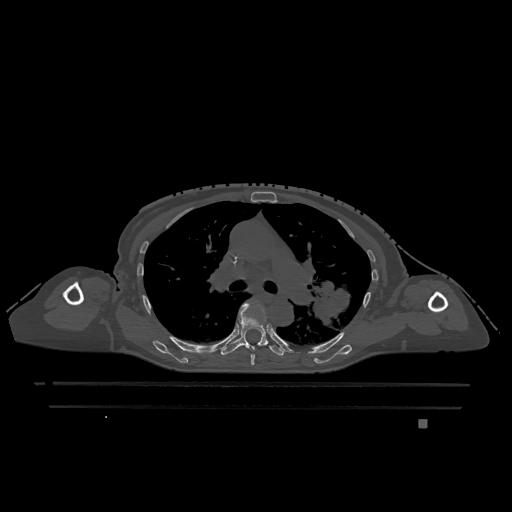
CT including the spine, one axial slice. Slice 806 of 1317 in the series (ordered by position). Bone window (W 1800 / L 400 HU). 0.5 mm slice thickness. 512 × 512 image matrix. Female patient, age 74 years. Case-level facts recorded for this patient, not image findings: primary cancer: lung.
Structures marked on this image (semi-automatically segmented with operator editing):
- T5 vertebra: bounding box (x1, y1, x2, y2) in pixels: (251, 354, 255, 366)
- T6 vertebra: (221, 303, 284, 356)